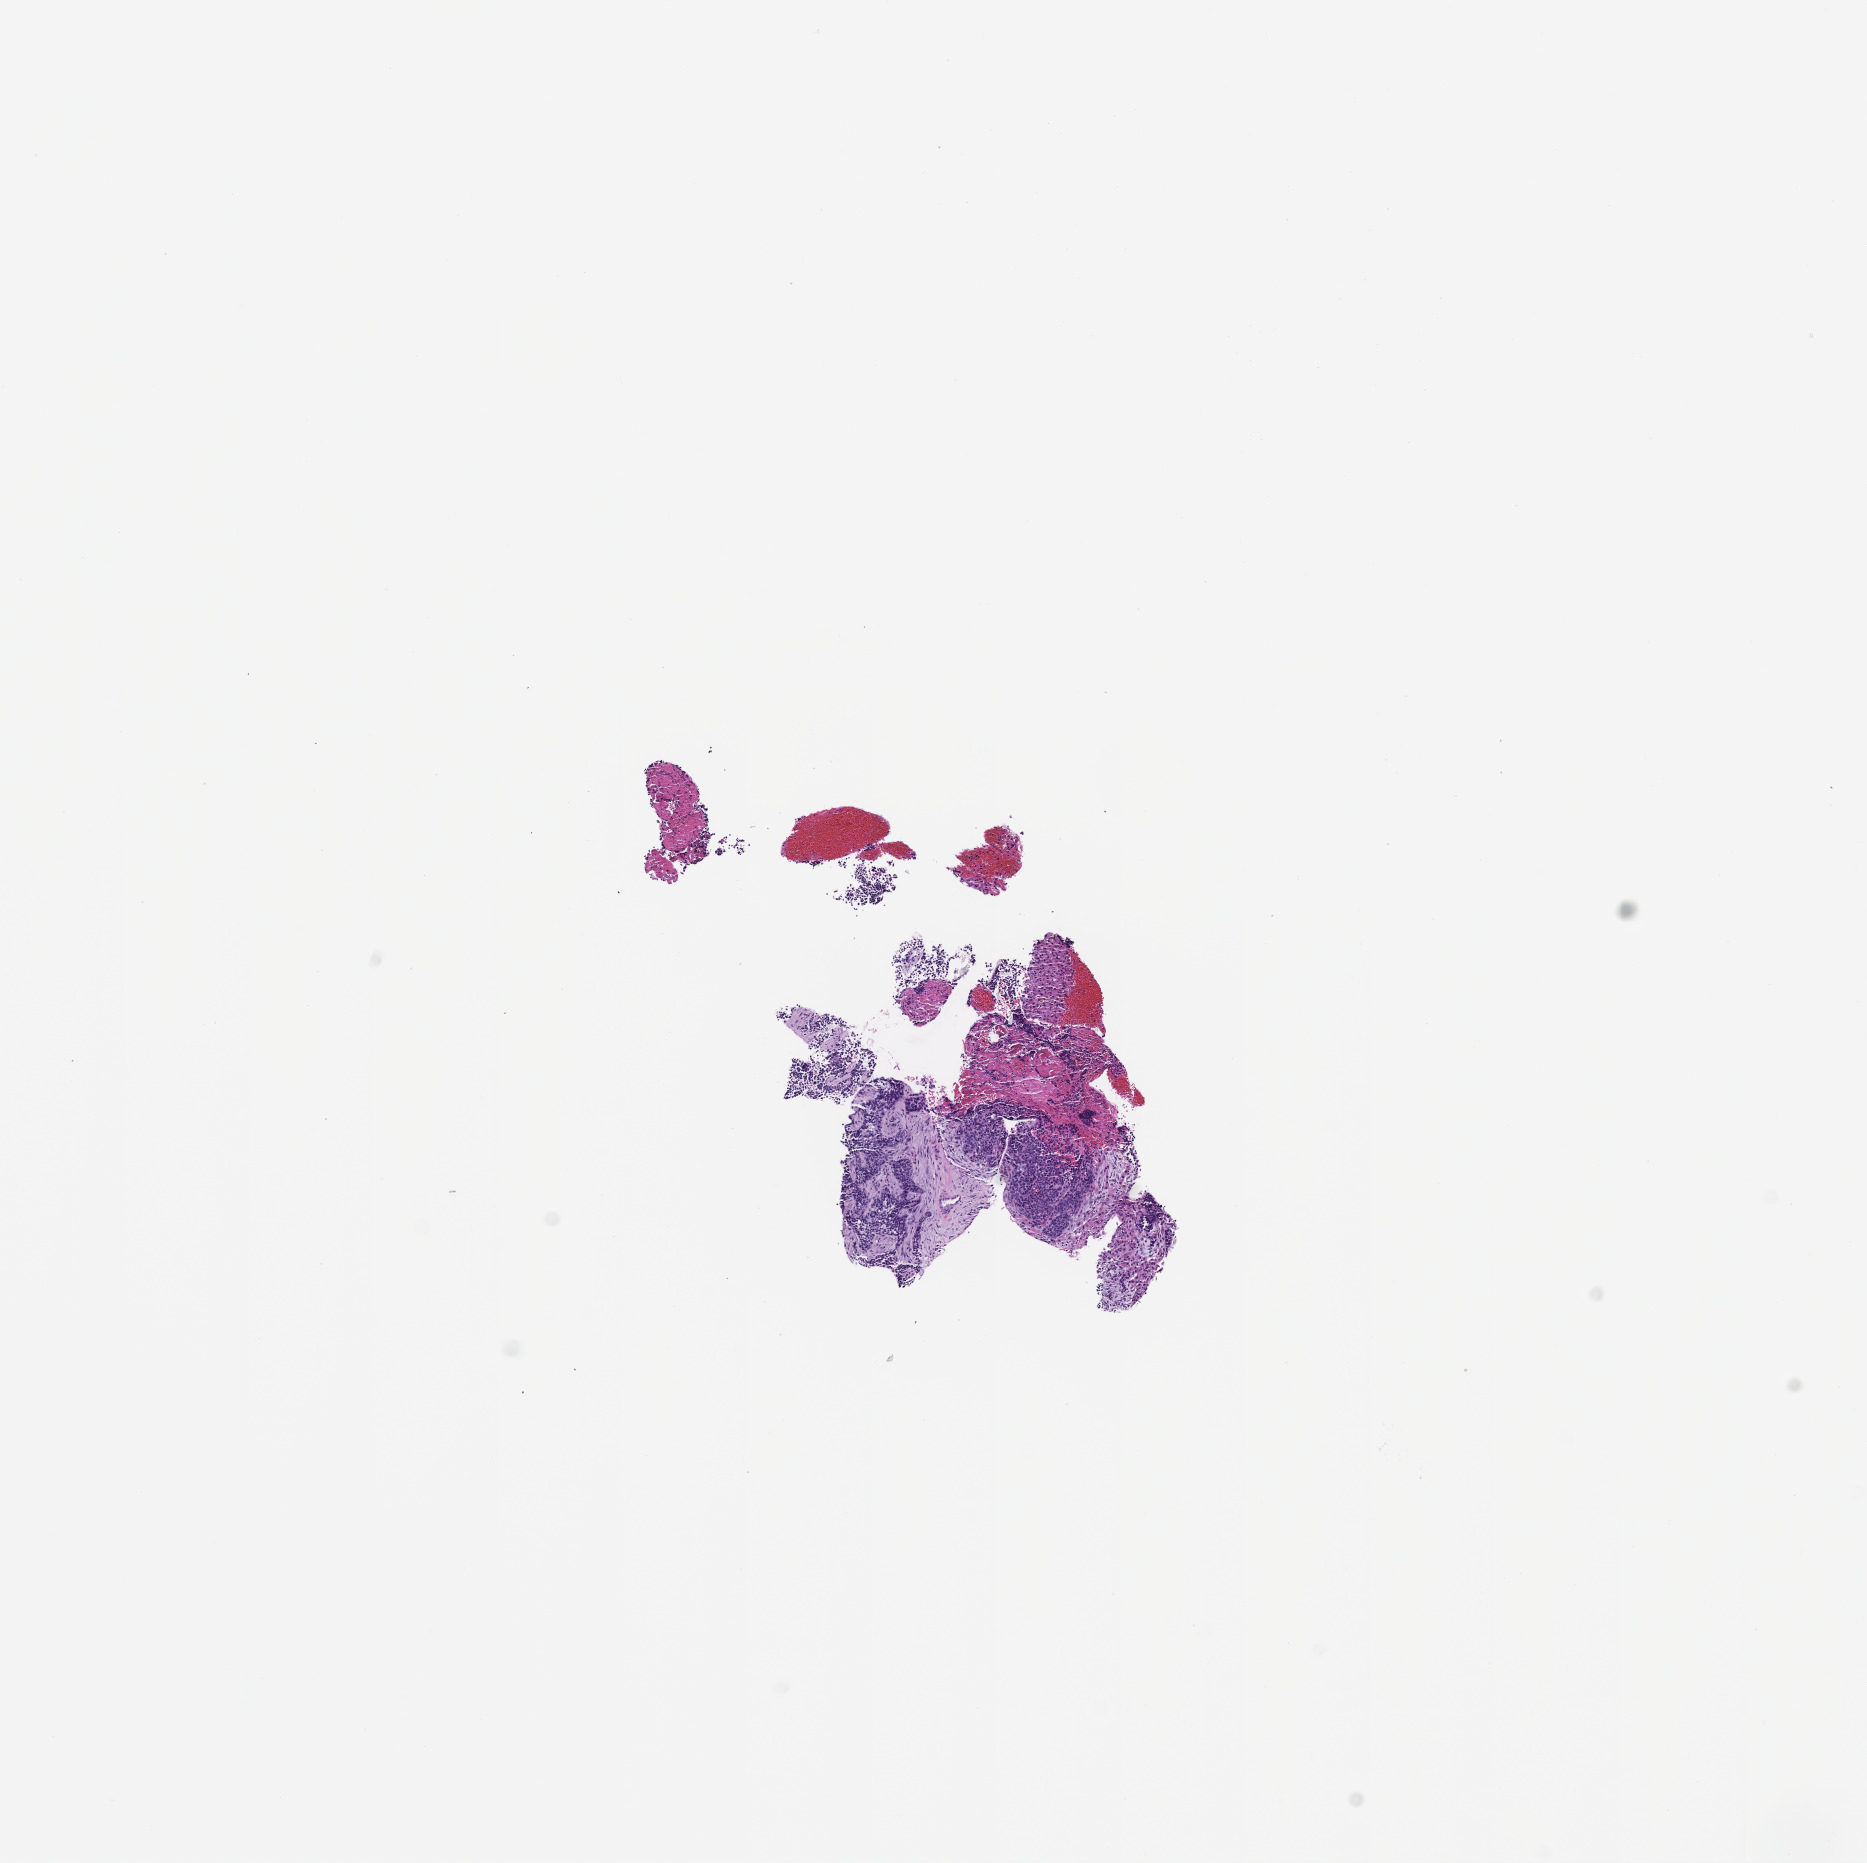
Whole-slide image, H&E stain, shown as a low-resolution overview of the whole scanned area (about 7.5 x 7.5 mm). FFPE section. Specimen time point: collected at baseline (before treatment). Patient sex: female.
* this section: metastatic tumor tissue
* patient diagnosis (primary): Adenocarcinoma of the Gastroesophageal Junction